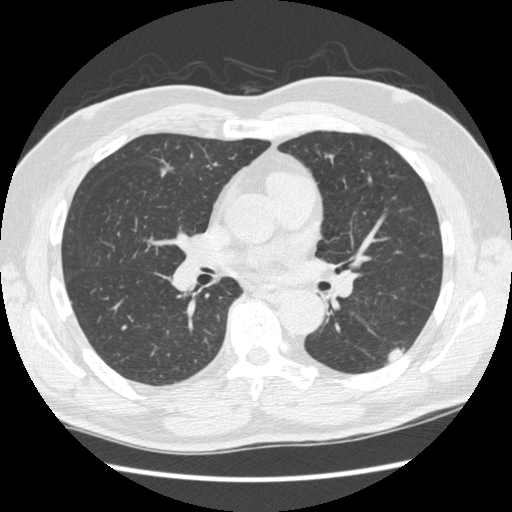
Low-dose screening chest CT, axial slice; first (baseline) screen; lung window (W 1500 / L -600 HU); 1.25 mm slice thickness; slice 121 of 267 in the series. Male participant, aged 74 years at enrolment. Former smoker at enrolment.
• Lesion marked by an expert reader, bounding box <372,324,414,368> (left, top, right, bottom; pixels).
• The screening reader recorded 3 non-calcified nodules or masses ≥4 mm on this exam; which of them this box marks is not recorded.
• Official screen result: positive, change unspecified: nodule(s) >= 4 mm or enlarging nodule(s), mass(es), or other non-specific abnormalities suspicious for lung cancer.
• Participant outcome: lung cancer diagnosed 384 days after this screen — squamous cell carcinoma, NOS, left lower lobe, well differentiated (G1), stage IA (AJCC 6th edition), 28 mm at pathology.